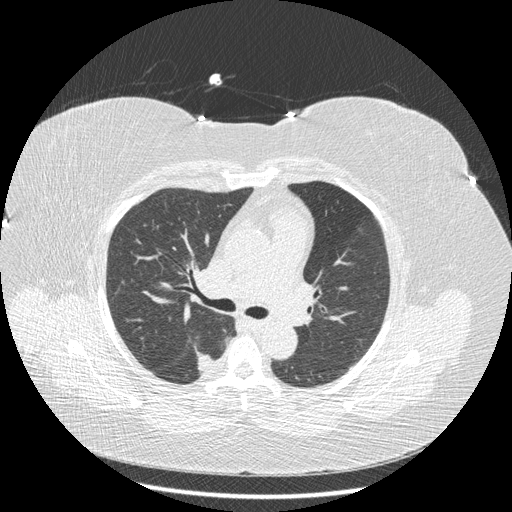
Low-dose screening chest CT, axial slice; baseline screening round; lung window (W 1500 / L -600 HU); 1.25 mm slice thickness; standard (soft-tissue) reconstruction kernel (STANDARD); slice 78 of 211 in the series. Female participant, aged 58 years at enrolment. Current smoker at enrolment.
Expert-annotated lung lesion, bounding box [x1, y1, x2, y2] px = [185, 346, 226, 382]. The exam's reader record, not a measurement of the box and not confirmed to be the same lesion: non-calcified nodule or mass ≥4 mm, right lower lobe, 15 × 10 mm, smooth margins, soft tissue attenuation. Official screen result: positive, change unspecified: nodule(s) >= 4 mm or enlarging nodule(s), mass(es), or other non-specific abnormalities suspicious for lung cancer. Participant outcome: lung cancer diagnosed 362 days after this screen — adenocarcinoma, NOS, right lower lobe, stage IB (AJCC 6th edition), 15 mm at pathology.